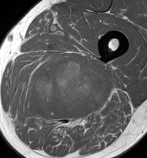
MRI of an extremity soft-tissue mass, one axial slice; position 71 of 86 along the scan axis; MR volume resampled by the dataset authors to the PET/CT grid (not the native acquisition matrix); 3.27 mm slice thickness; 147 × 158 image matrix, field of view 144 × 154 mm. Male patient. From the clinical record (not read from this slice): histological type: undifferentiated pleomorphic liposarcoma; grade: high; site of the primary tumour: left thigh.
Annotated regions visible in this slice (expert contour drawn on MRI and transferred to this co-registered scan by the dataset authors):
- gross tumour volume including surrounding oedema: bounding box <21,56,113,127> (left, top, right, bottom; pixels)
- gross tumour volume (mass): <30,60,111,118>